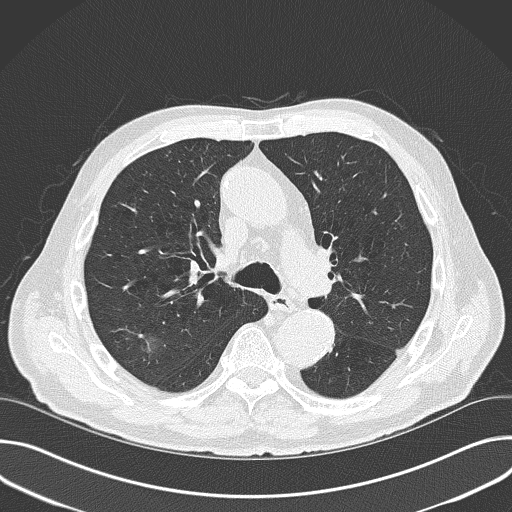
Low-dose screening chest CT, axial slice; baseline screening round; lung window (W 1500 / L -600 HU); 2 mm slice thickness; lung (sharp) reconstruction kernel (B50f); slice 107 of 177 in the series. Male participant, aged 74 years at enrolment. Former smoker at enrolment.
Expert reader's lesion annotation, bounding box (x1, y1, x2, y2) in pixels: (126, 324, 173, 369). The screening reader recorded 3 non-calcified nodules or masses ≥4 mm on this exam (right upper lobe, right upper lobe, right middle lobe); which of them this box marks is not recorded. Lung cancer was diagnosed 215 days after this screen: small cell carcinoma, NOS, right upper lobe, stage IV (AJCC 6th edition), 15 mm at pathology.